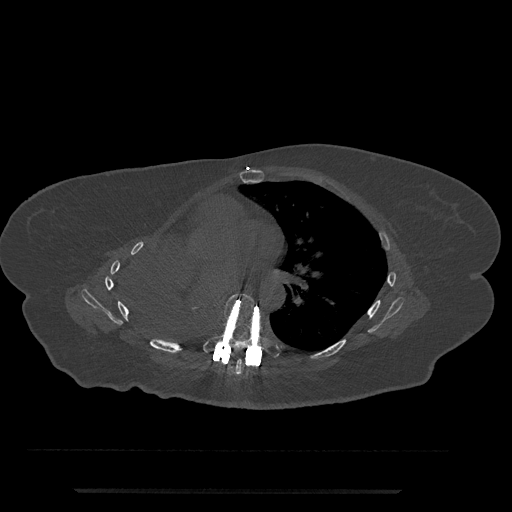
CT including the spine, one axial slice. Slice 453 of 797 in the series (ordered by position). Bone window (W 1800 / L 400 HU). 512 × 512 image matrix. Patient: female, 51 years. From the clinical record (not read from this slice): primary cancer: neuro; vertebrae with lytic lesions (as recorded): T8.
Annotated regions visible in this slice (semi-automatically segmented with operator editing):
- T6 vertebra: bounding box [x1, y1, x2, y2] px = [222, 359, 243, 376]
- T7 vertebra: [203, 293, 280, 358]